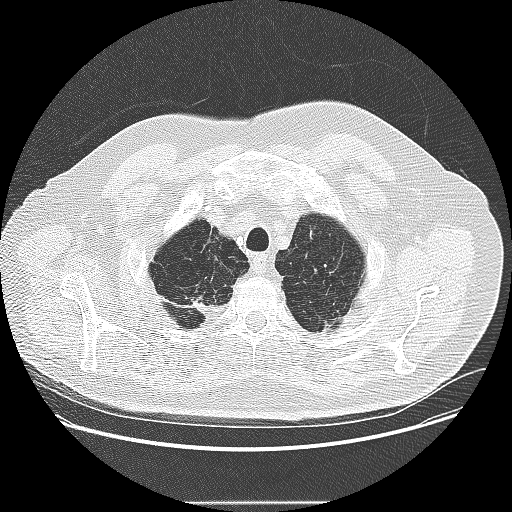
Low-dose screening chest CT, one axial slice; position 219 of 265 along the scan axis; reconstruction kernel LUNG; 120 kVp; lung window (W 1500 / L -600 HU); 512 × 512 image matrix.
Outlined on this slice (outlined manually by an expert reader):
- lesion 1 (tumor, upper lobe of left lung): bounding box (x1, y1, x2, y2) in pixels: (310, 228, 315, 238)